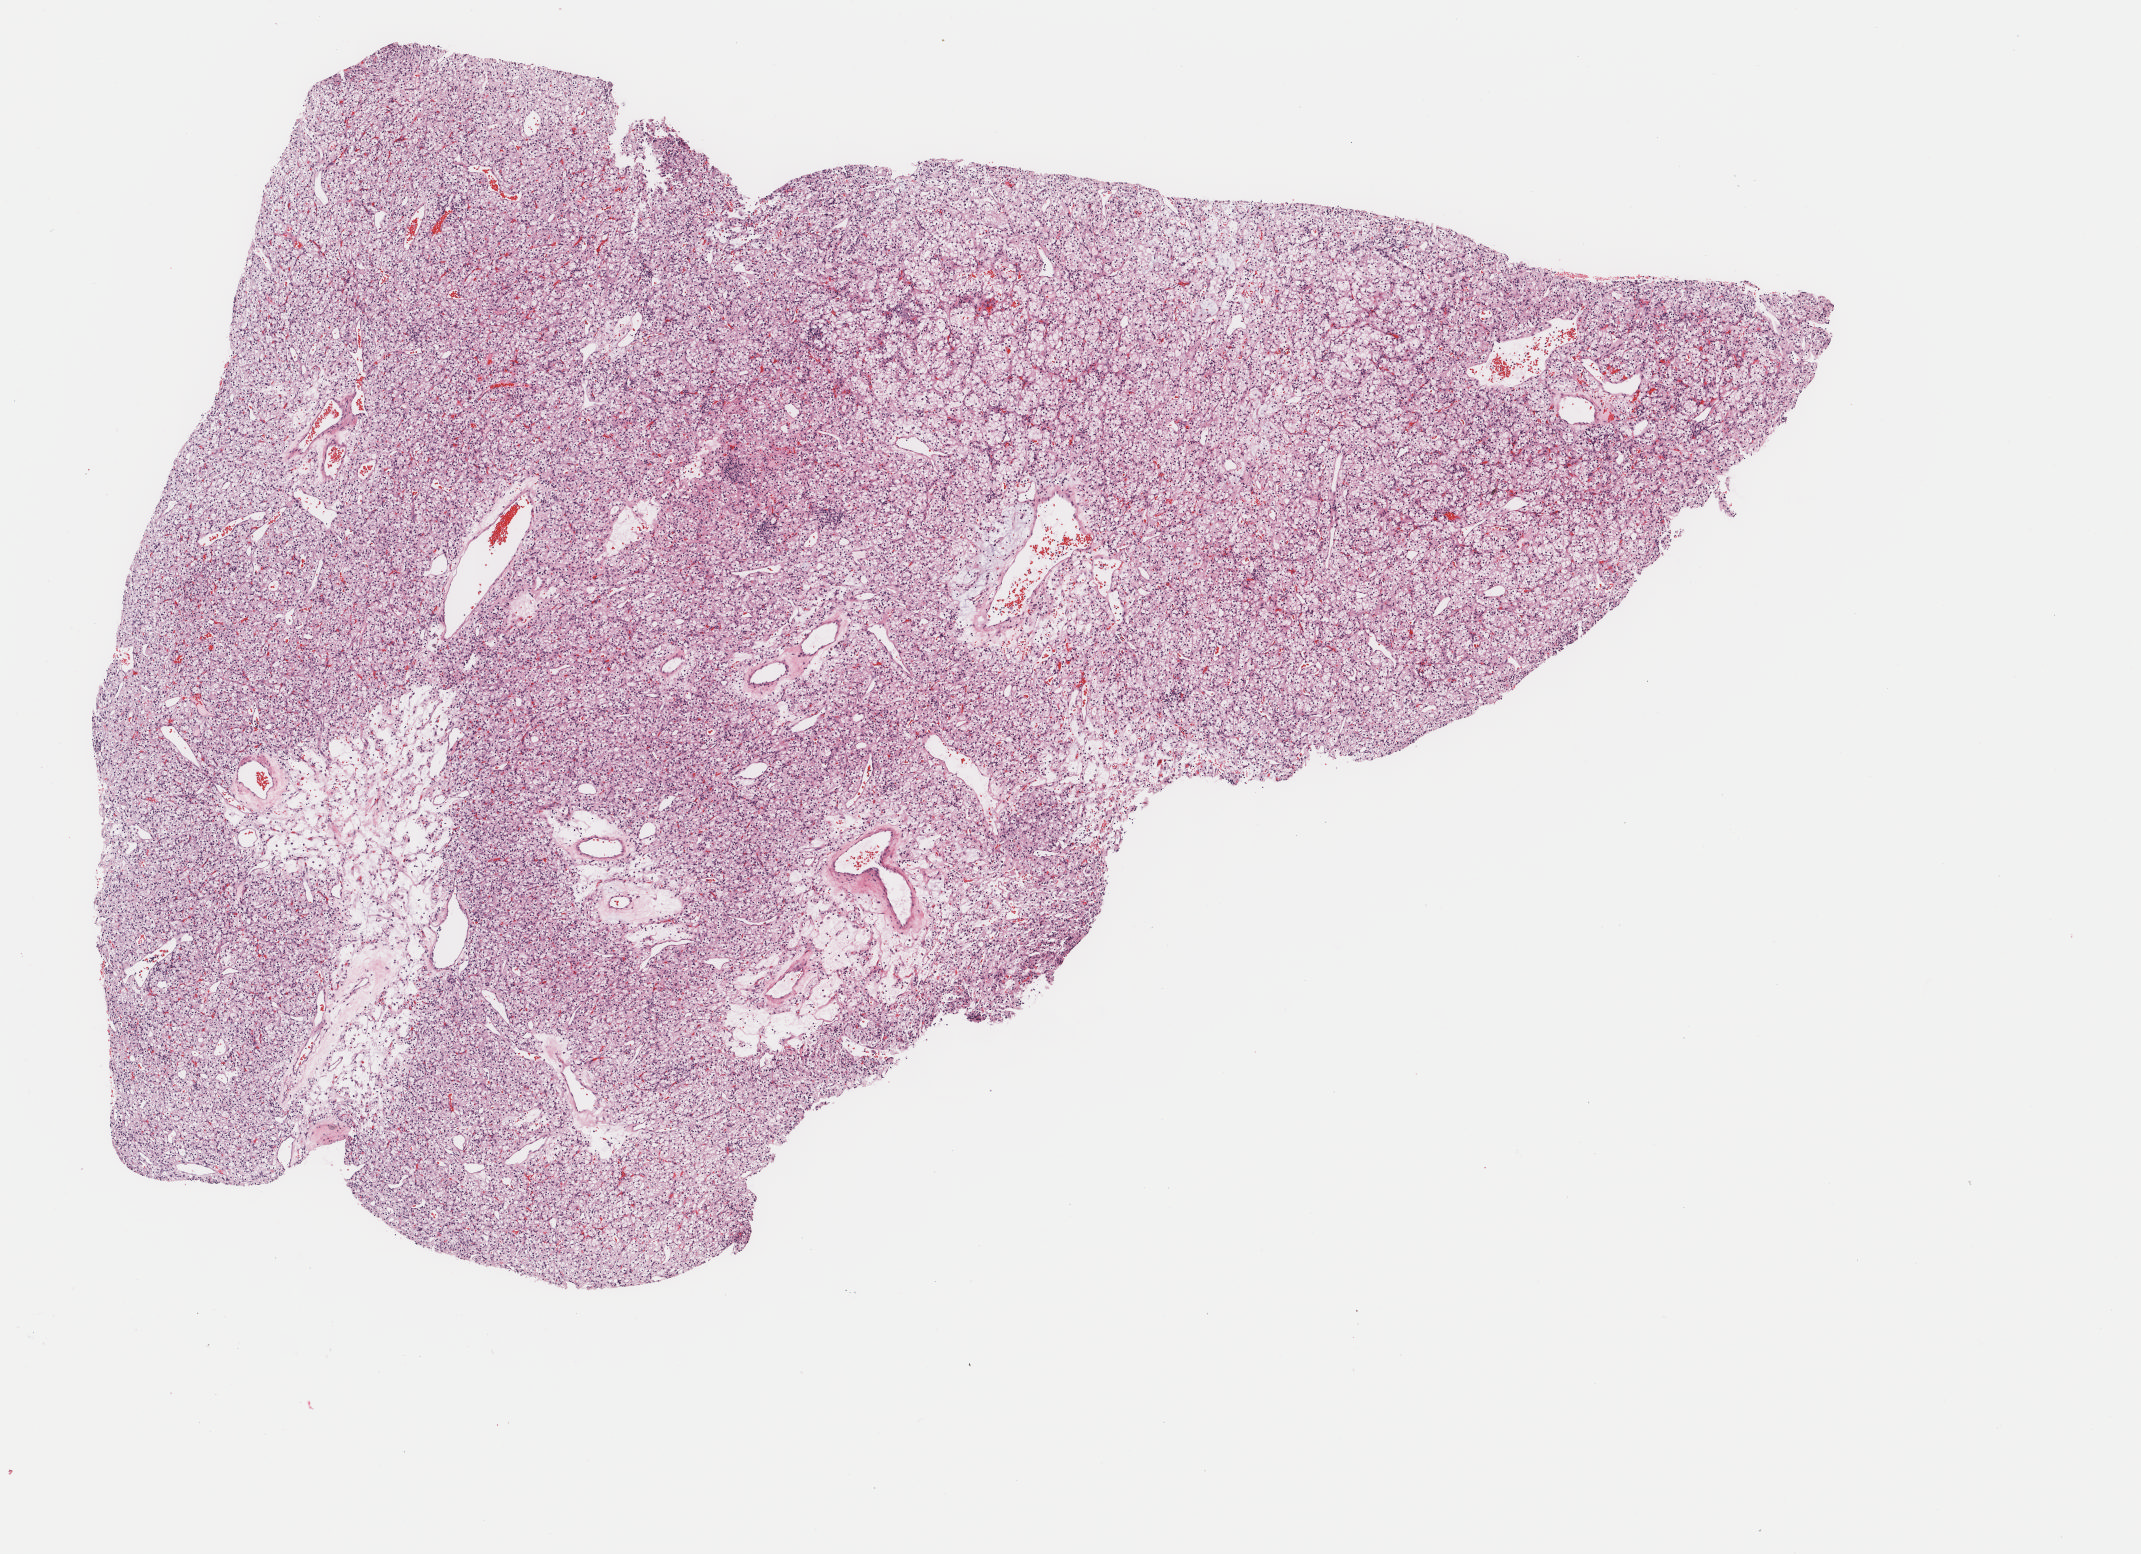
Digitized Hematoxylin and eosin (H&E) stained tissue section (whole slide), low-resolution overview of the scanned area, about 8.5 x 6.2 mm (from a 40x scan), frozen section from the bottom of the tissue portion, kidney, primary tumour sample. Patient: male, age at initial diagnosis 74 years.
Diagnosis: Clear cell adenocarcinoma, NOS.